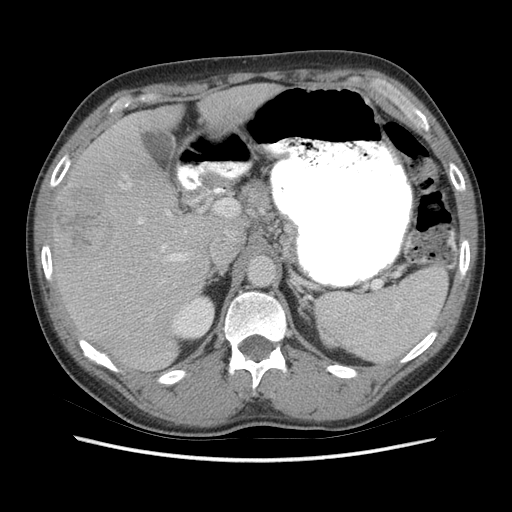
Contrast-enhanced abdominal CT (liver protocol), one axial slice; reconstruction kernel STANDARD; soft-tissue window (W 400 / L 40 HU); 2.5 mm slice thickness; 512 × 512 image matrix, field of view 360 × 360 mm. Case-level facts recorded for this patient, not image findings: diagnosis: hepatocellular carcinoma (patient treated with transarterial chemoembolisation; whether this scan precedes or follows treatment is not stated here); TNM stage (as recorded): Stage-IIIA; Child-Pugh class: A; tumour nodularity: multinodular.
Outlined on this slice (semi-automatically segmented with operator editing):
- liver parenchyma outside the tumour (the mass and vessels are separate outlines, so this box may not span the whole liver): box from (x=52, y=84) to (x=280, y=370) px
- mass: (x=59, y=189)–(x=113, y=257)
- liver vessels: (x=121, y=176)–(x=188, y=262)